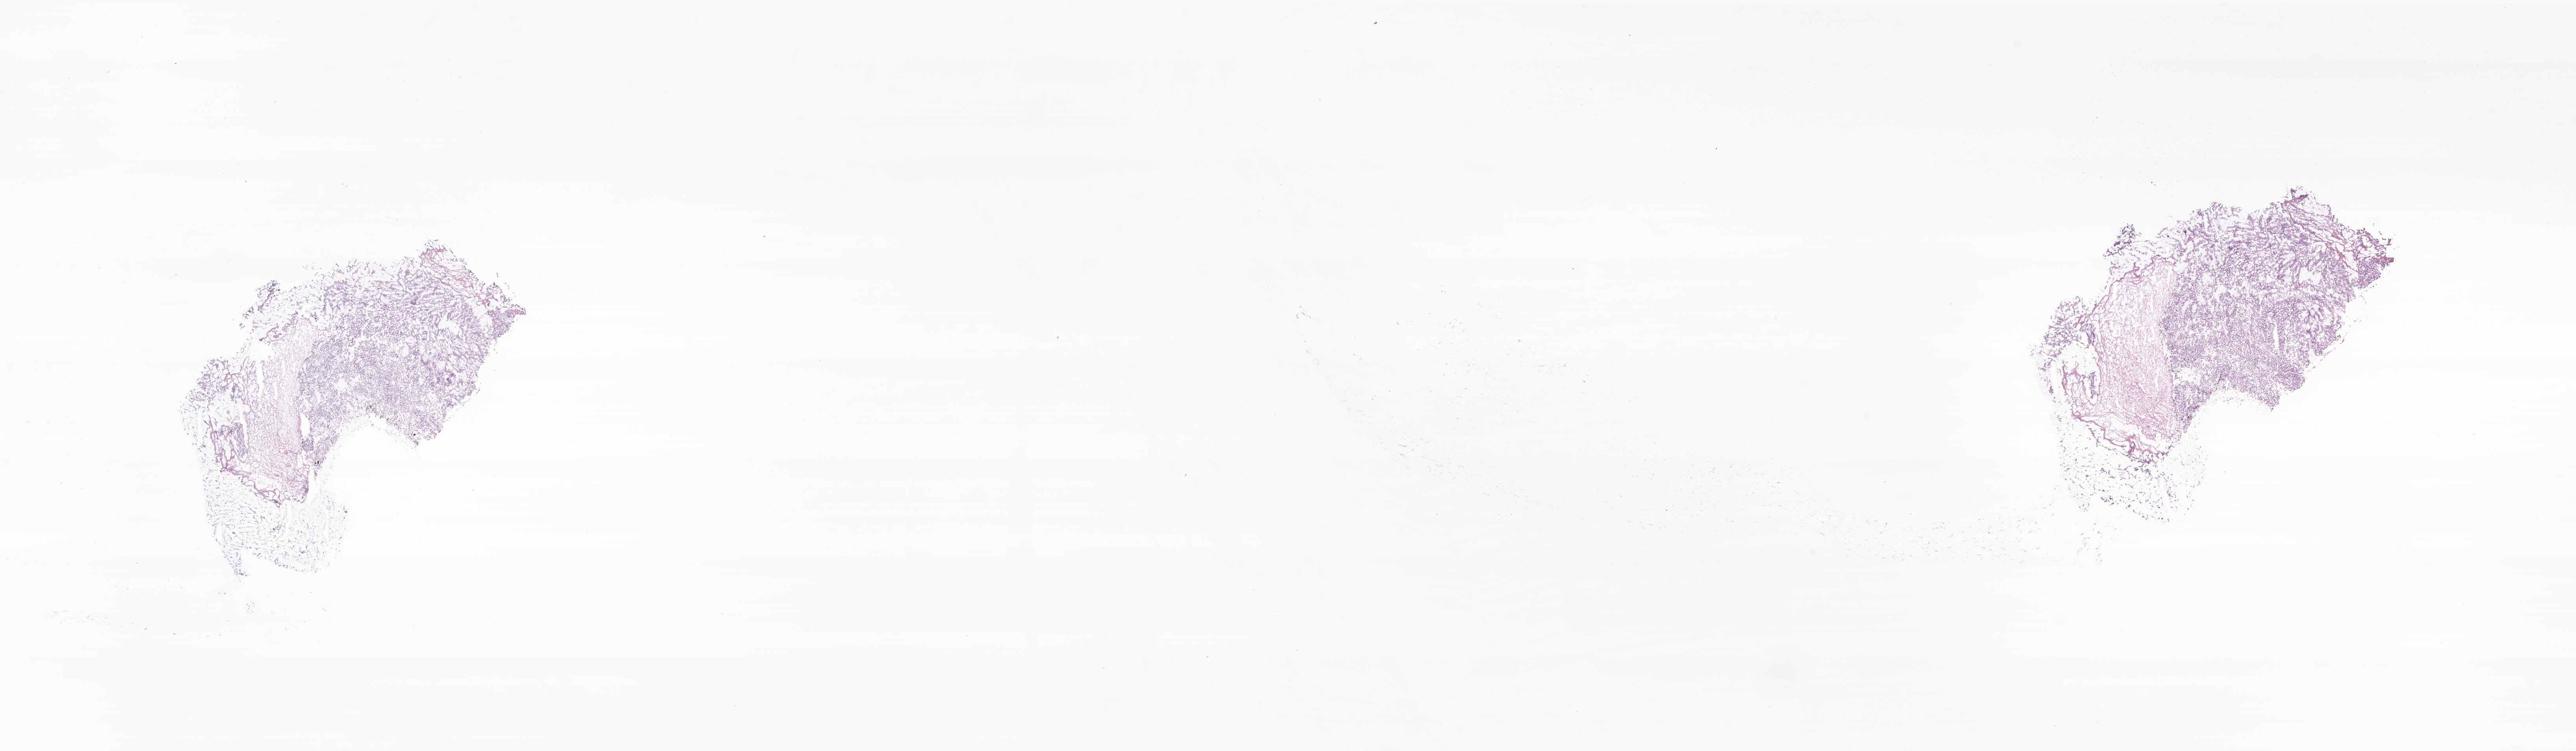
Hematoxylin and eosin (H&E) whole-slide image of tumor tissue from the pancreas, whole scanned area (about 27.6 x 8.1 mm) shown as a low-resolution overview; frozen section (OCT-embedded). Male patient, age 149 months.
Diagnosis (ICD-O-3 morphology term): Solid pseudopapillary neoplasm of pancreas.